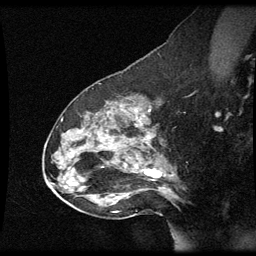
Breast MRI (dynamic contrast-enhanced), one sagittal slice; slice 37 of 60 in the series (ordered by position); dynamic contrast-enhanced series, image 2 of 3 at this slice position (ordered by acquisition); 1.5 T; TE 4.2 ms, TR 8.9 ms; 2 mm slice thickness; 256 × 256 image matrix, field of view 200 × 200 mm. Patient: female, 49 years. From the clinical record (not read from this slice): setting: breast cancer imaged before/during neoadjuvant chemotherapy; receptor status: HR-positive, HER2-negative.
Structures marked on this image (semi-automatic segmentation, software-assisted and operator-edited):
- analysis volume of interest (the breast-tissue region the enhancement analysis was run in; not a lesion): box from (x=46, y=92) to (x=177, y=205) px
- tumour enhancement mask (voxels above the 70 % enhancement threshold inside the analysis volume of interest): (x=136, y=110)–(x=148, y=175)